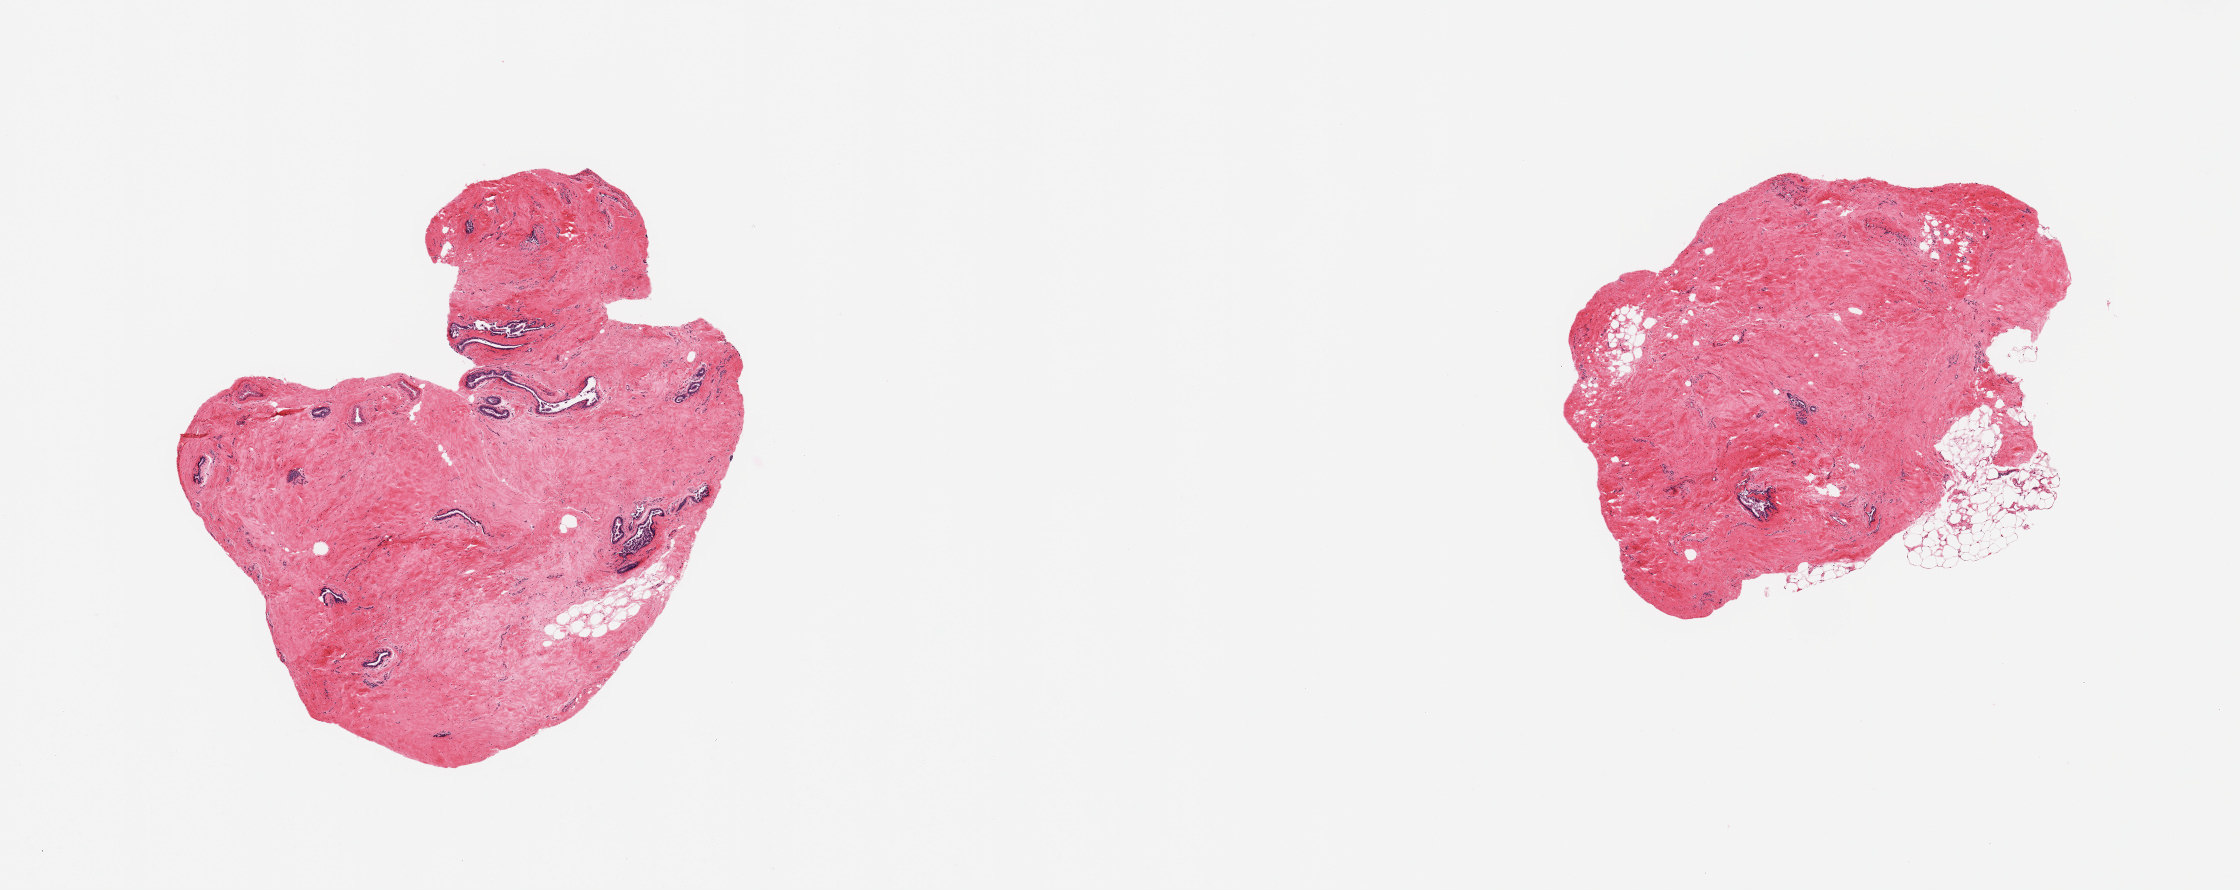
H&E whole-slide image — low-resolution overview of the scanned area, about 17.7 x 7.0 mm (acquisition: 20x scan). PAXgene-fixed, paraffin-embedded tissue. Target tissue: breast. Tissue donor sample. Male donor.
Review note (as recorded): 2 pieces; predominantly dense fibrous stroma with minimal adipose tissue and several scattered ductal structures.